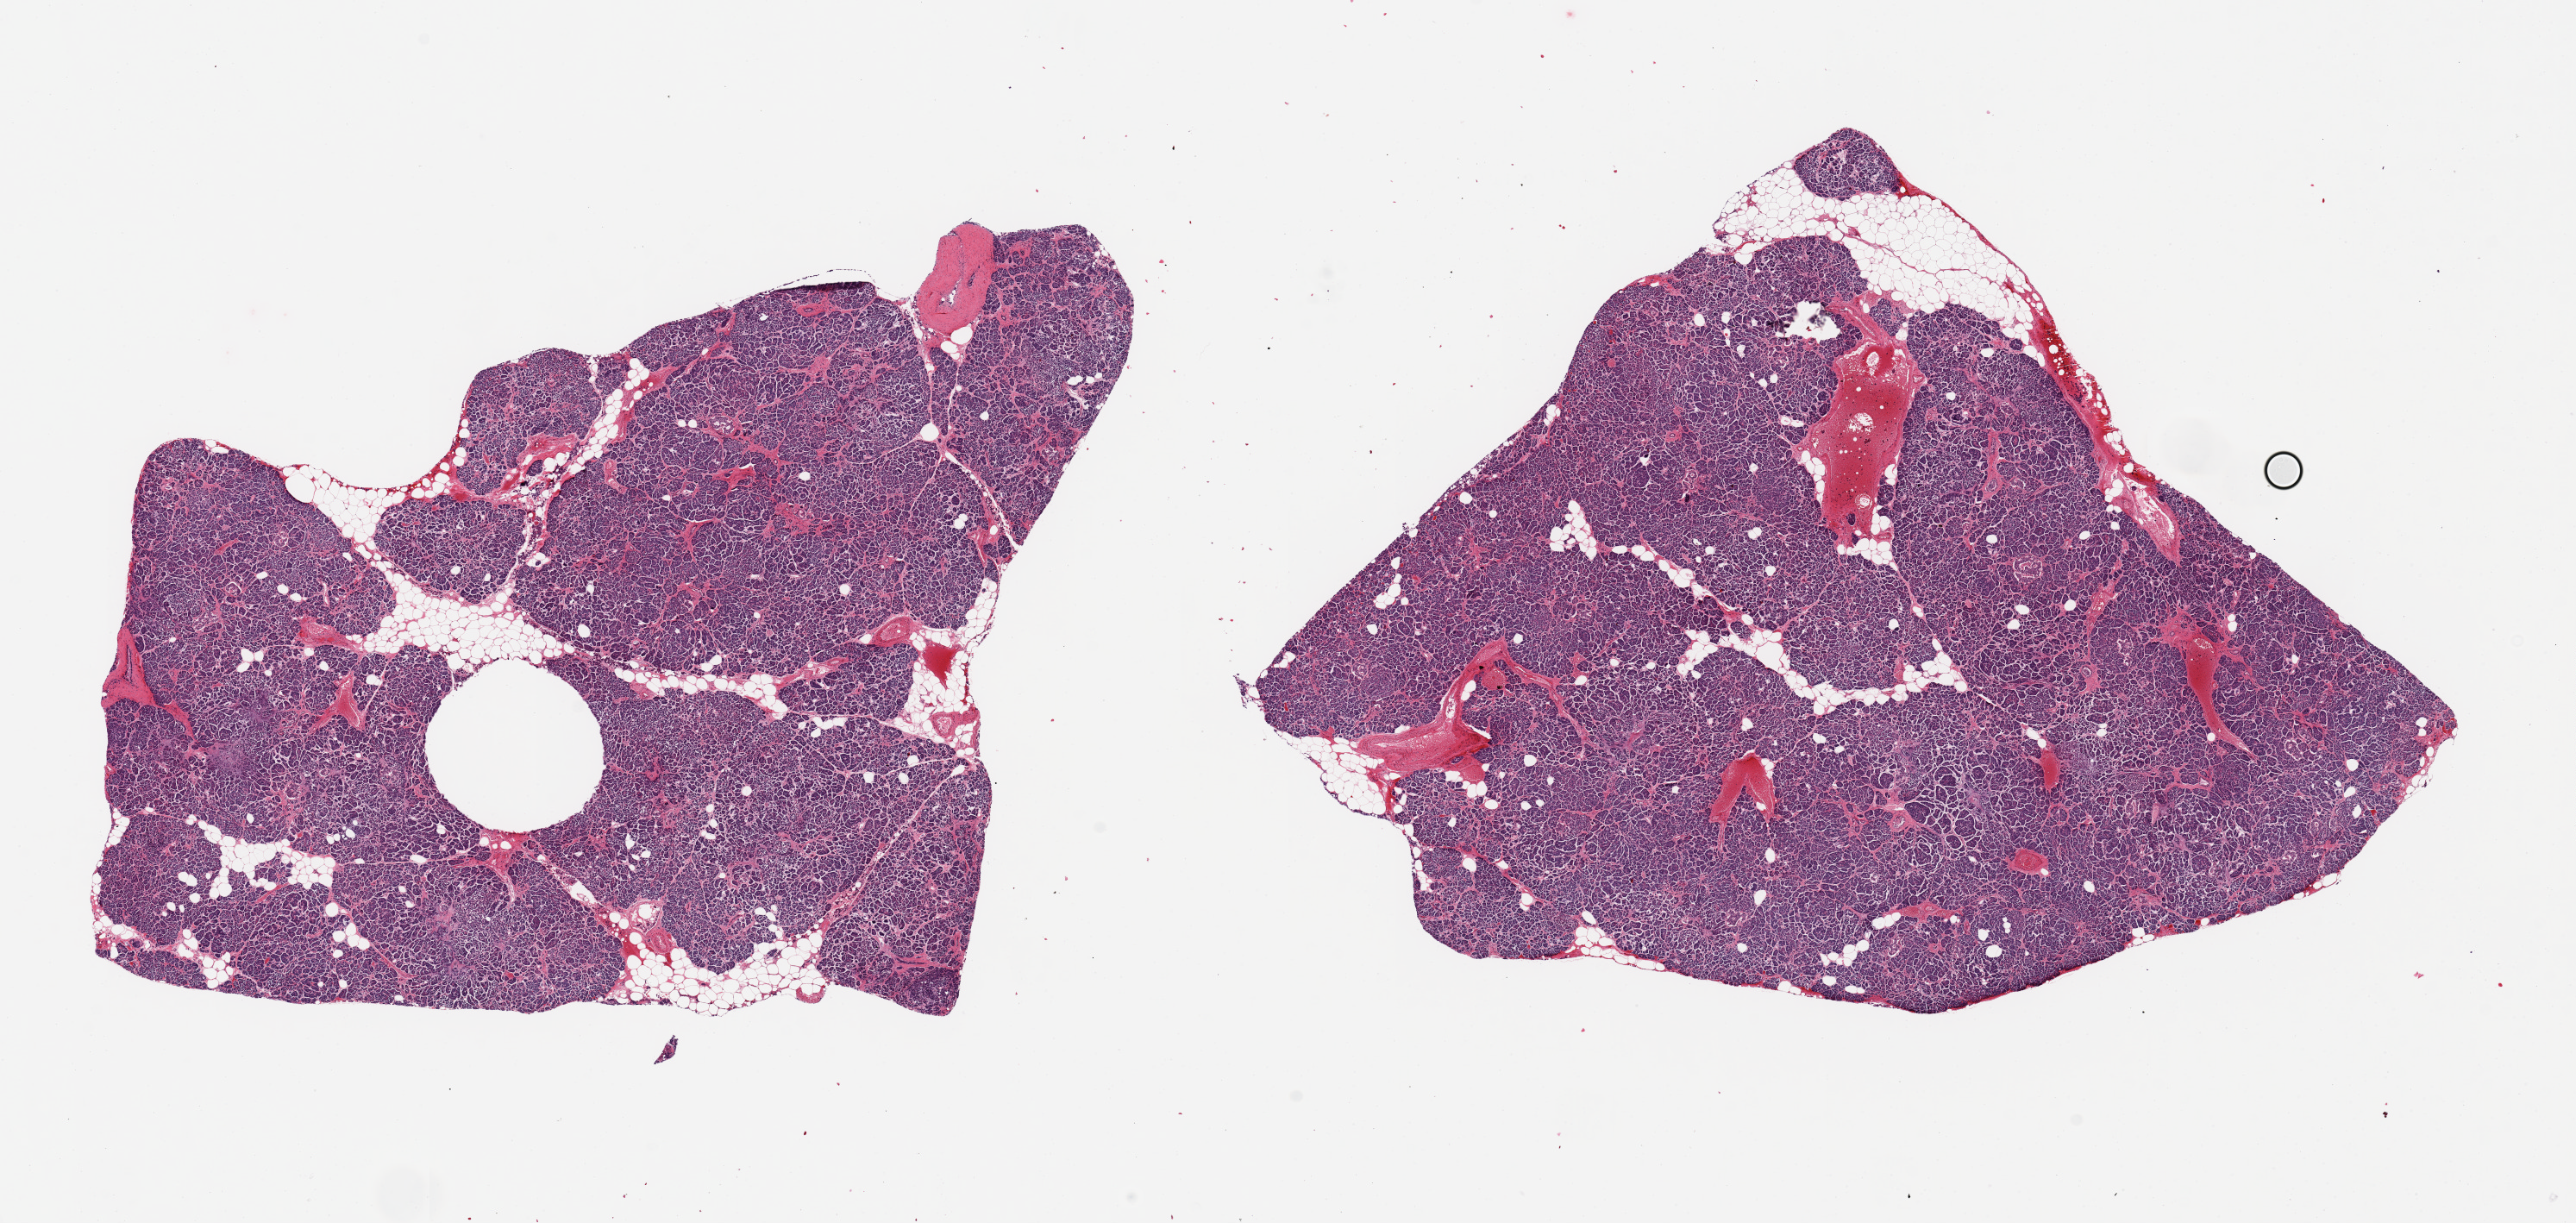
Whole-slide image, haematoxylin and eosin stain, brightfield, low-resolution overview of the scanned area, about 23.6 x 11.2 mm (acquisition: 20x scan), PAXgene-fixed paraffin-embedded (PFPE) section, section of pancreas (target tissue), donor tissue sample. Donor: male.
• pathologist's review note for this sample: 2 pieces, 9.5x7 & 9x8mm; minimal adherent fat, poorly preserved